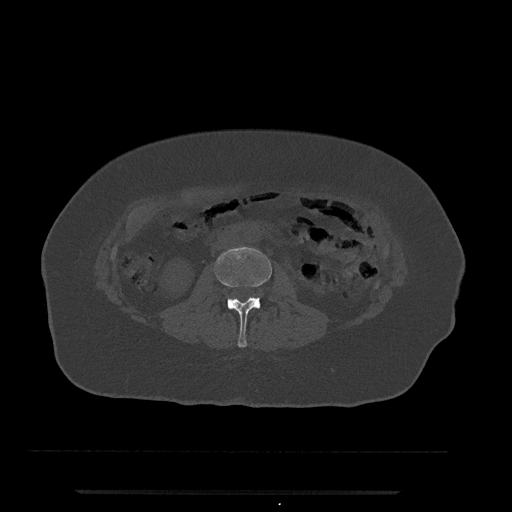
CT including the spine, one axial slice. Slice 21 of 797 in the series (ordered by position). Bone window (W 1800 / L 400 HU). 0.5 mm slice thickness. 512 × 512 image matrix. Patient: female, 51 years. Case-level facts recorded for this patient, not image findings: primary cancer: neuro.
Outlined on this slice (semi-automatic segmentation, software-assisted and operator-edited):
- L2 vertebra: bounding box [x1, y1, x2, y2] px = [214, 247, 272, 347]